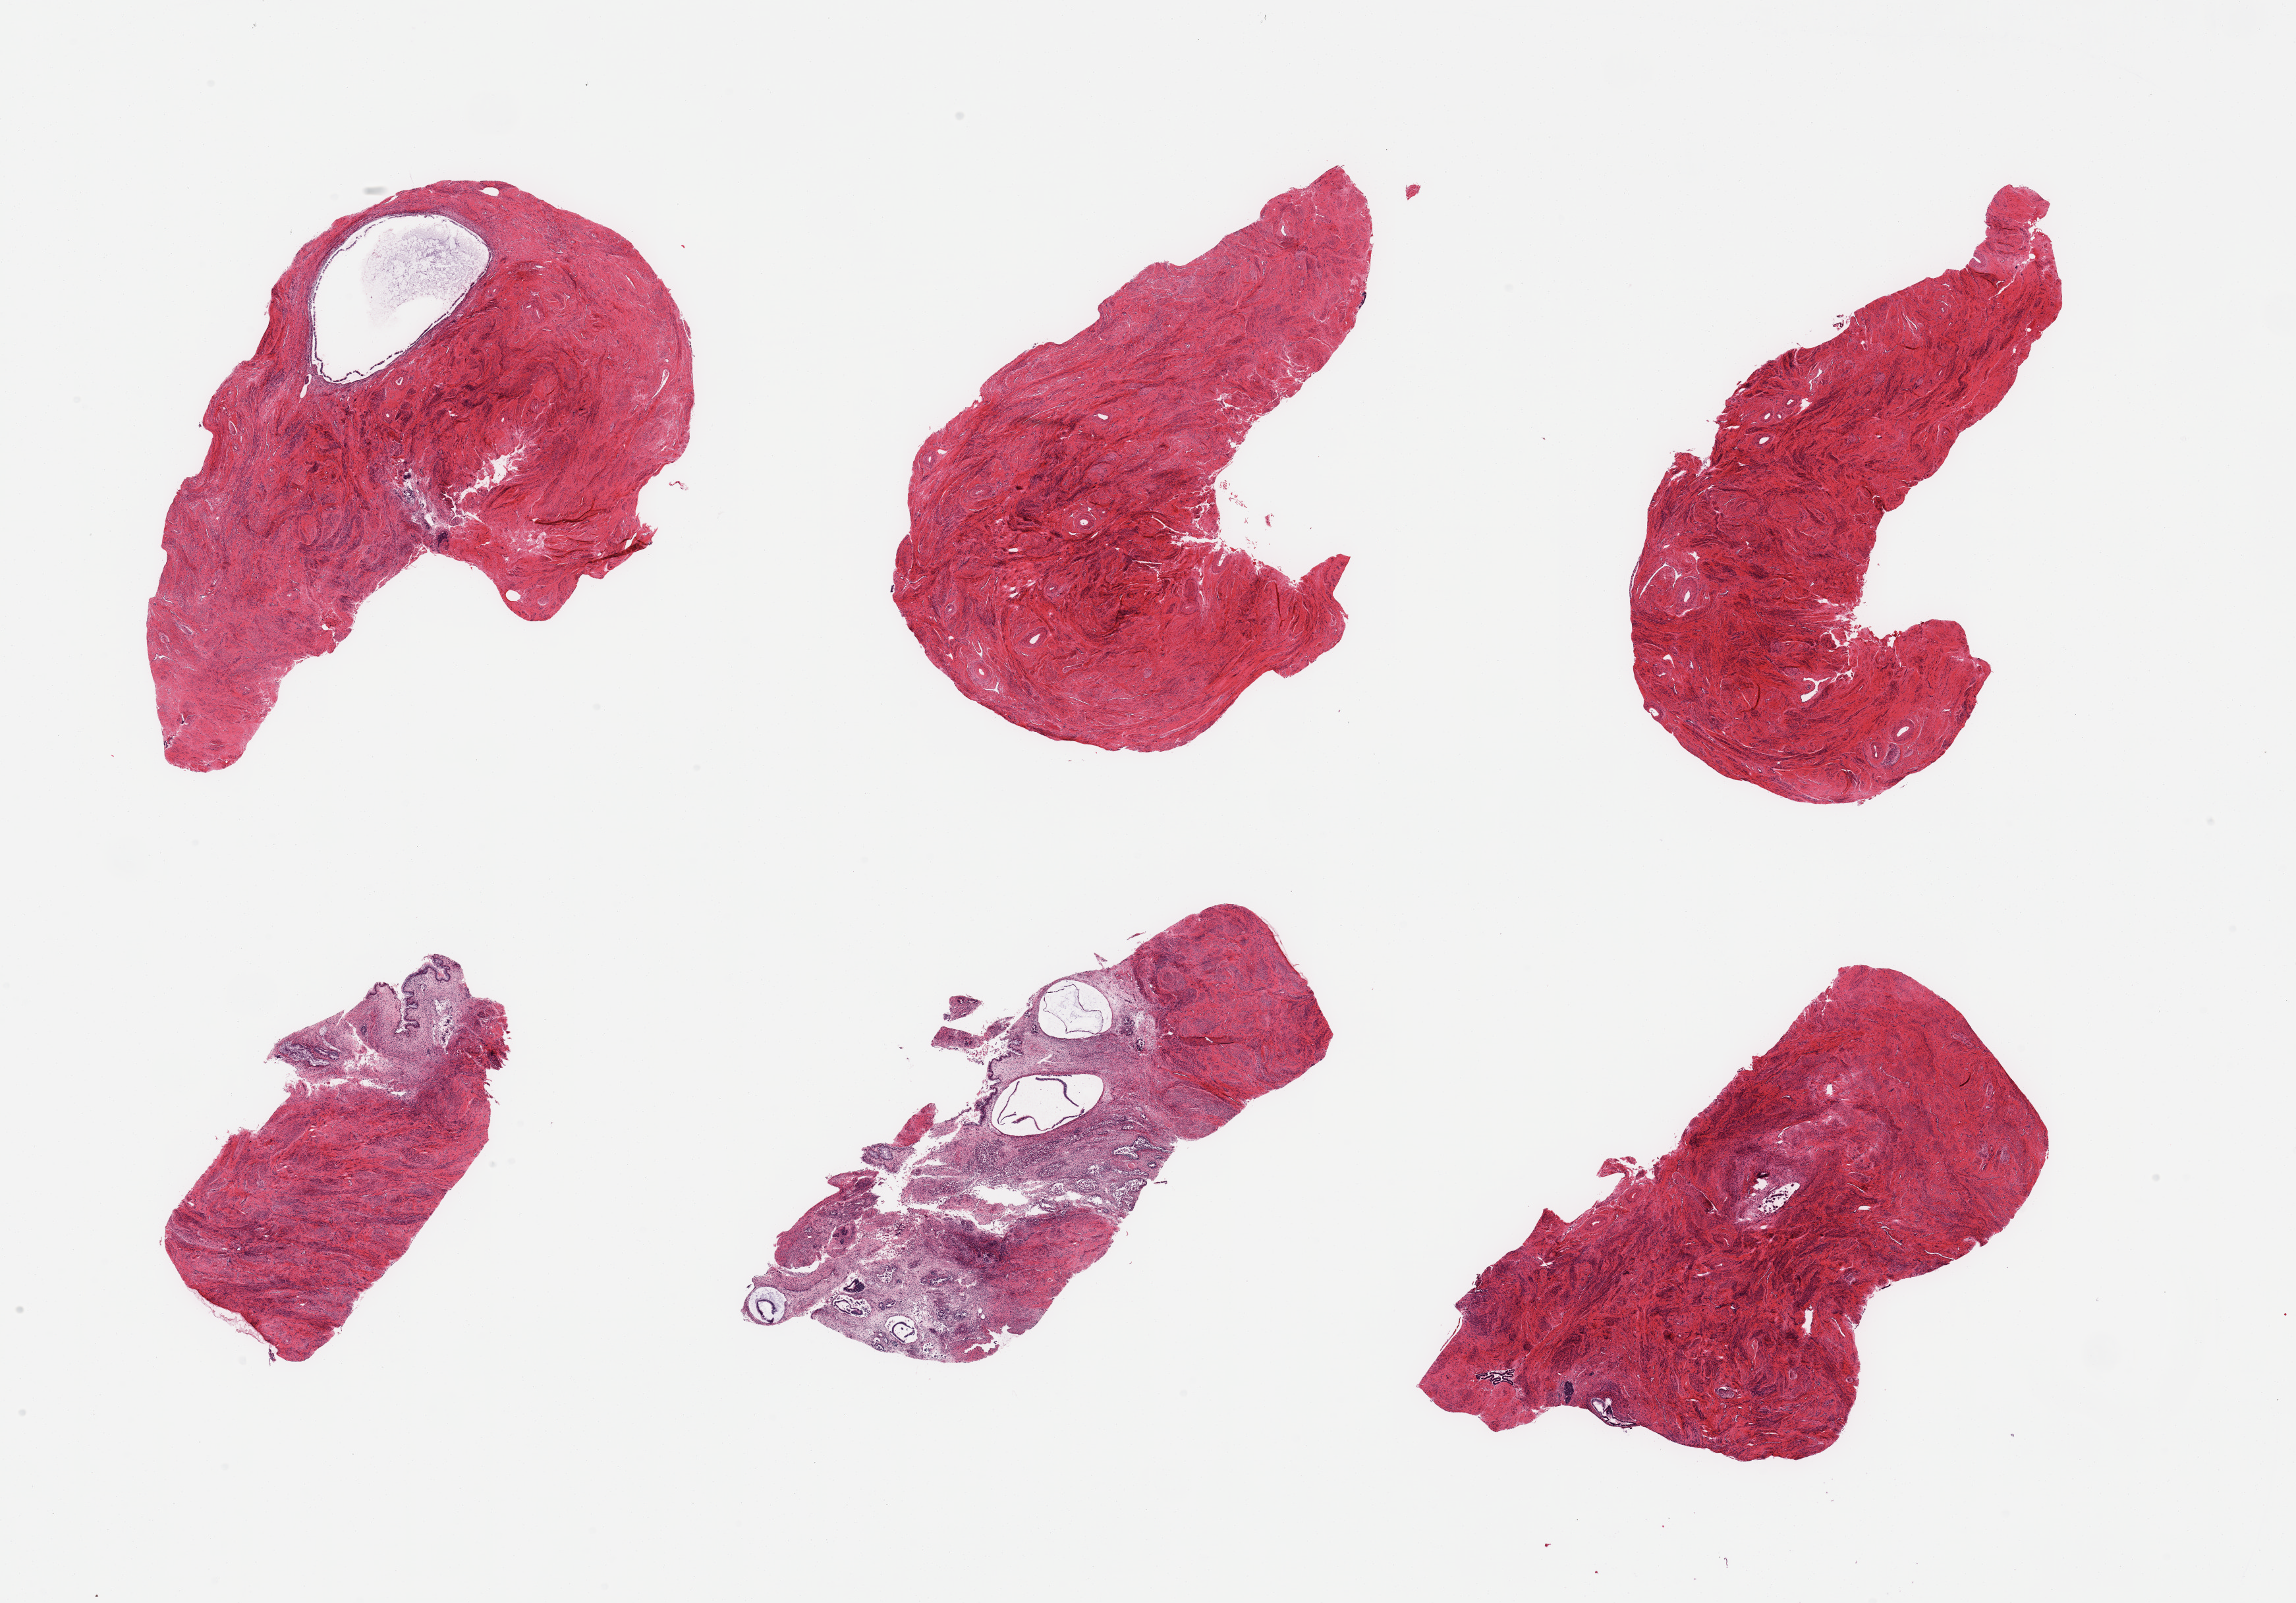
H&E whole-slide image, brightfield, whole scanned area (about 27.6 x 19.2 mm, acquisition: 20x scan) shown as a low-resolution overview; PAXgene-fixed, paraffin-embedded tissue; target tissue: vagina; donor tissue sample.
Pathologist's review note for this sample: 6 pieces; NOT vagina; cervical canal with autolyzed mucous glands and cysts.